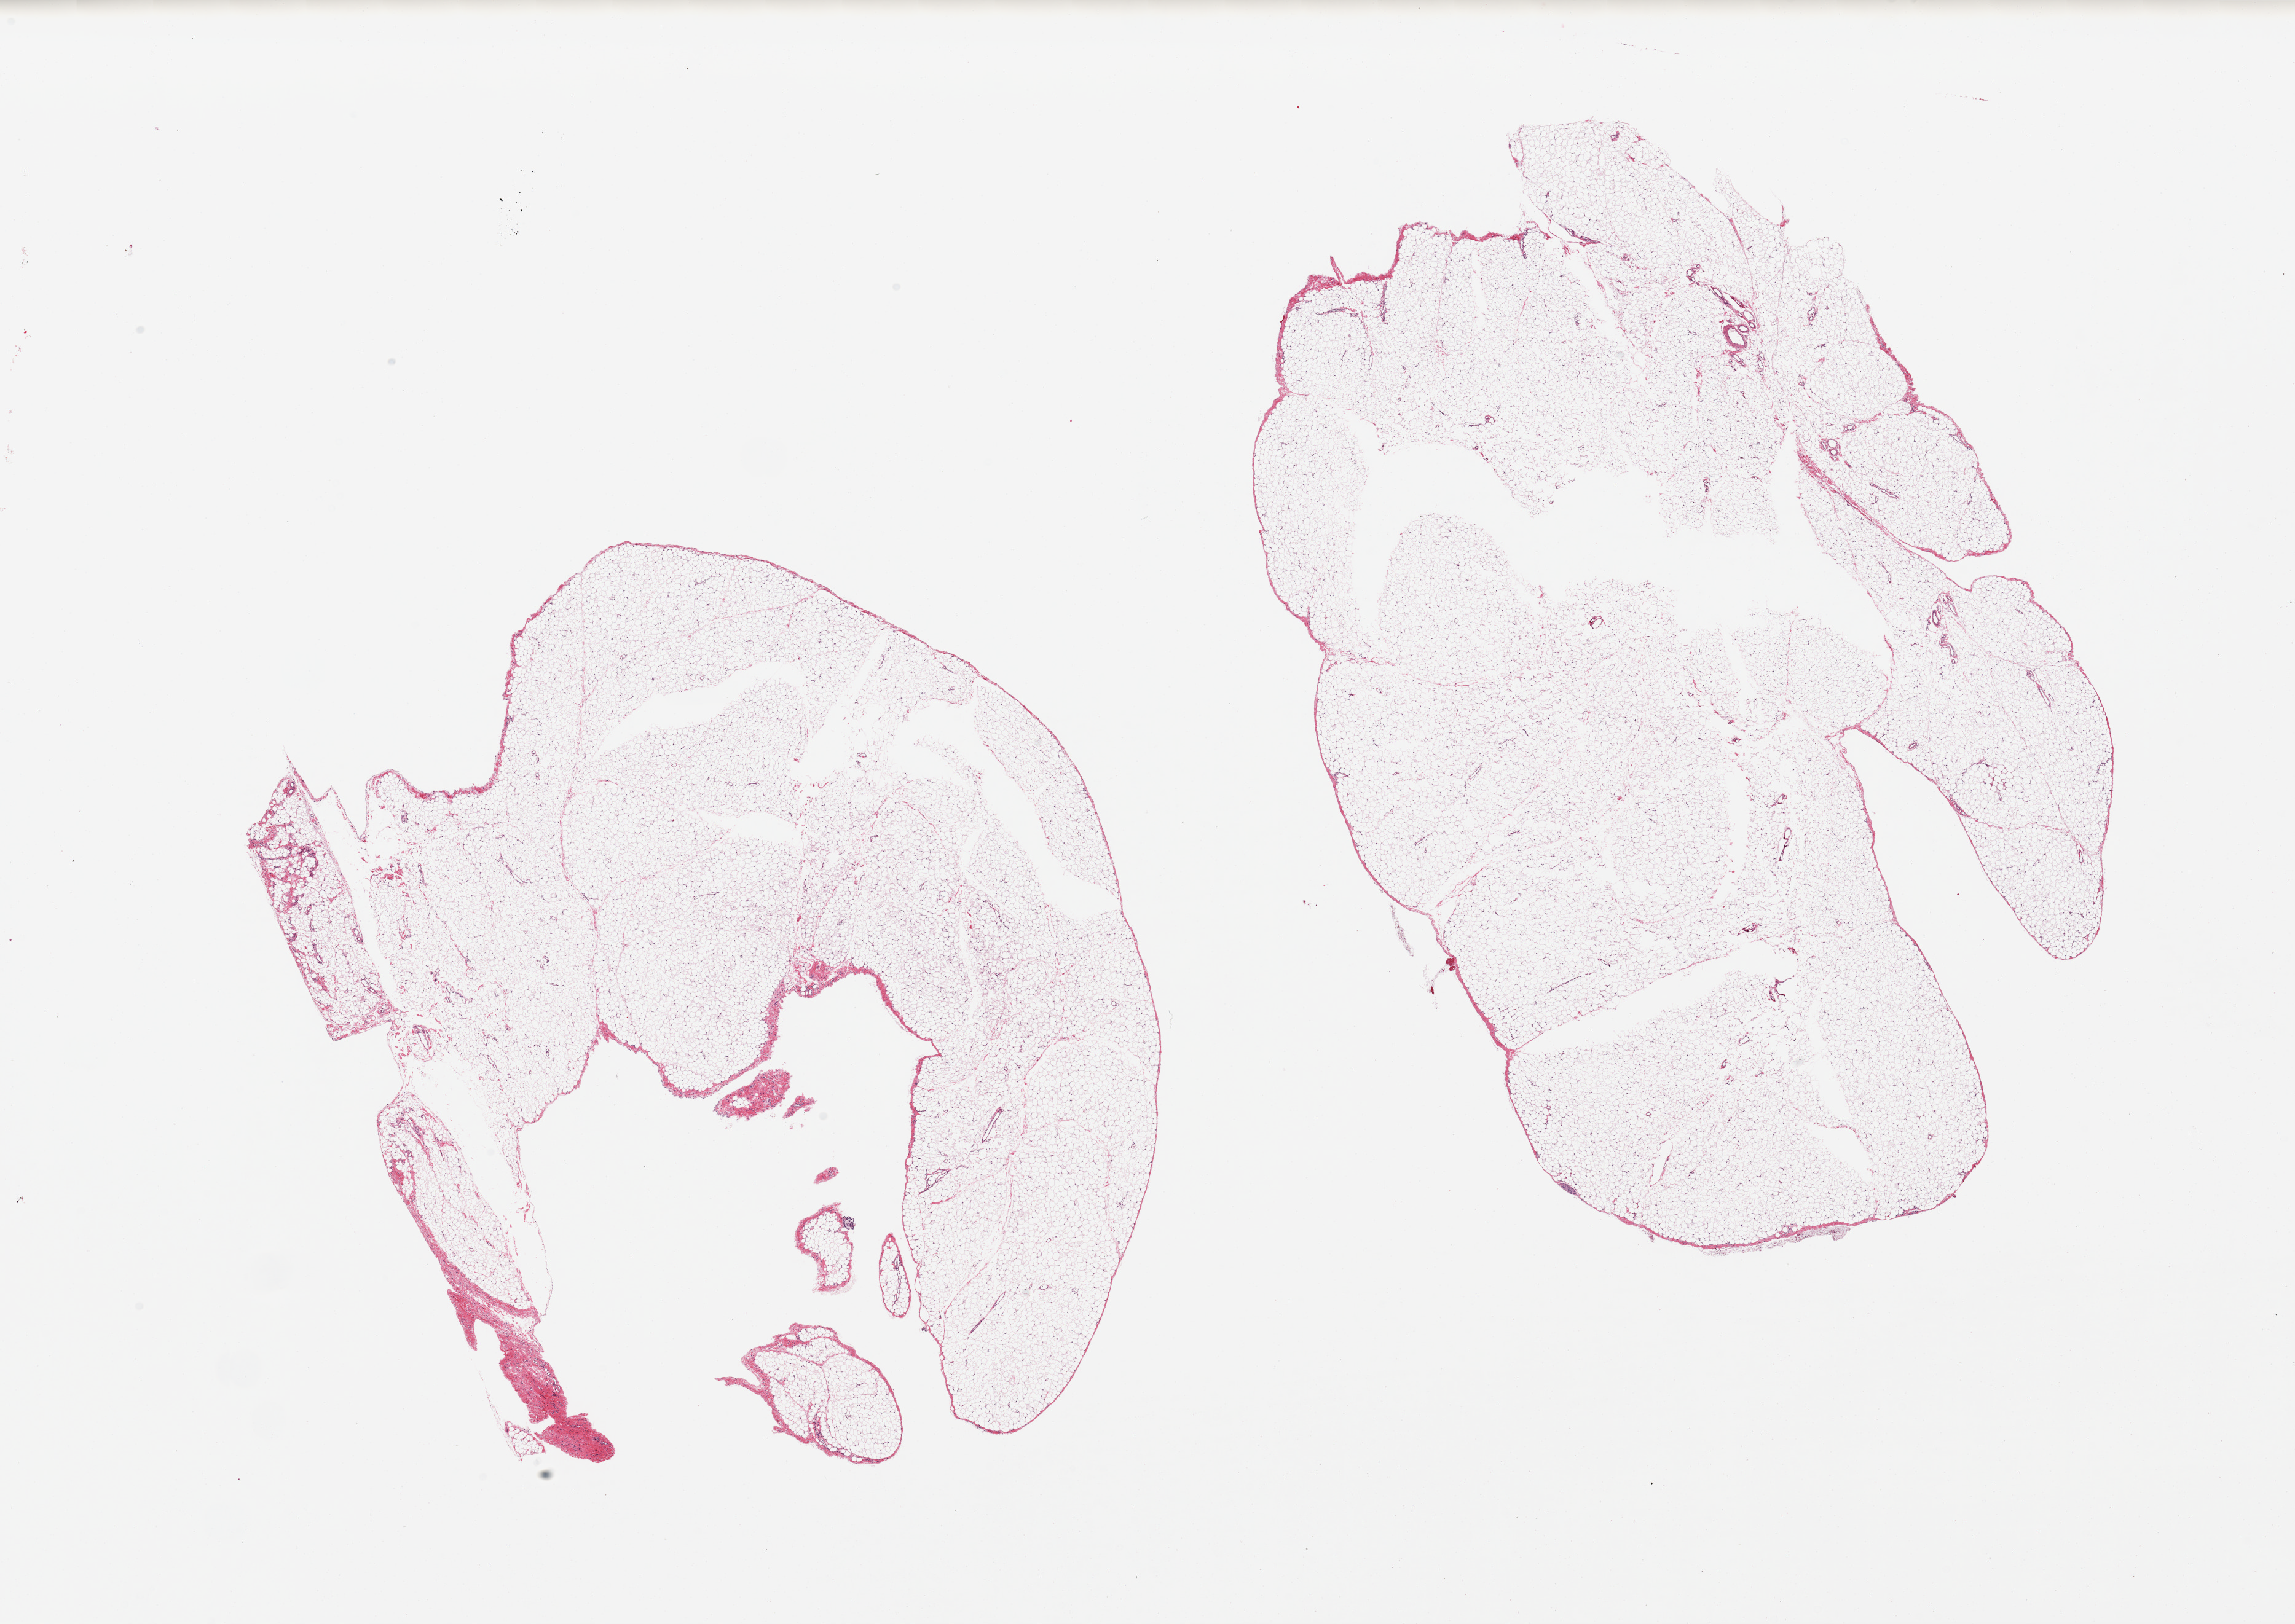
Hematoxylin and eosin (H&E) whole-slide image, brightfield — whole scanned area (about 29.5 x 20.9 mm) shown as a low-resolution overview. PAXgene-fixed paraffin-embedded (PFPE) section. Section of omentum (target tissue). Donor tissue sample. Donor: female.
Reviewer comment on this tissue sample: 2 pieces, minimal fibrous/vascular tissue.